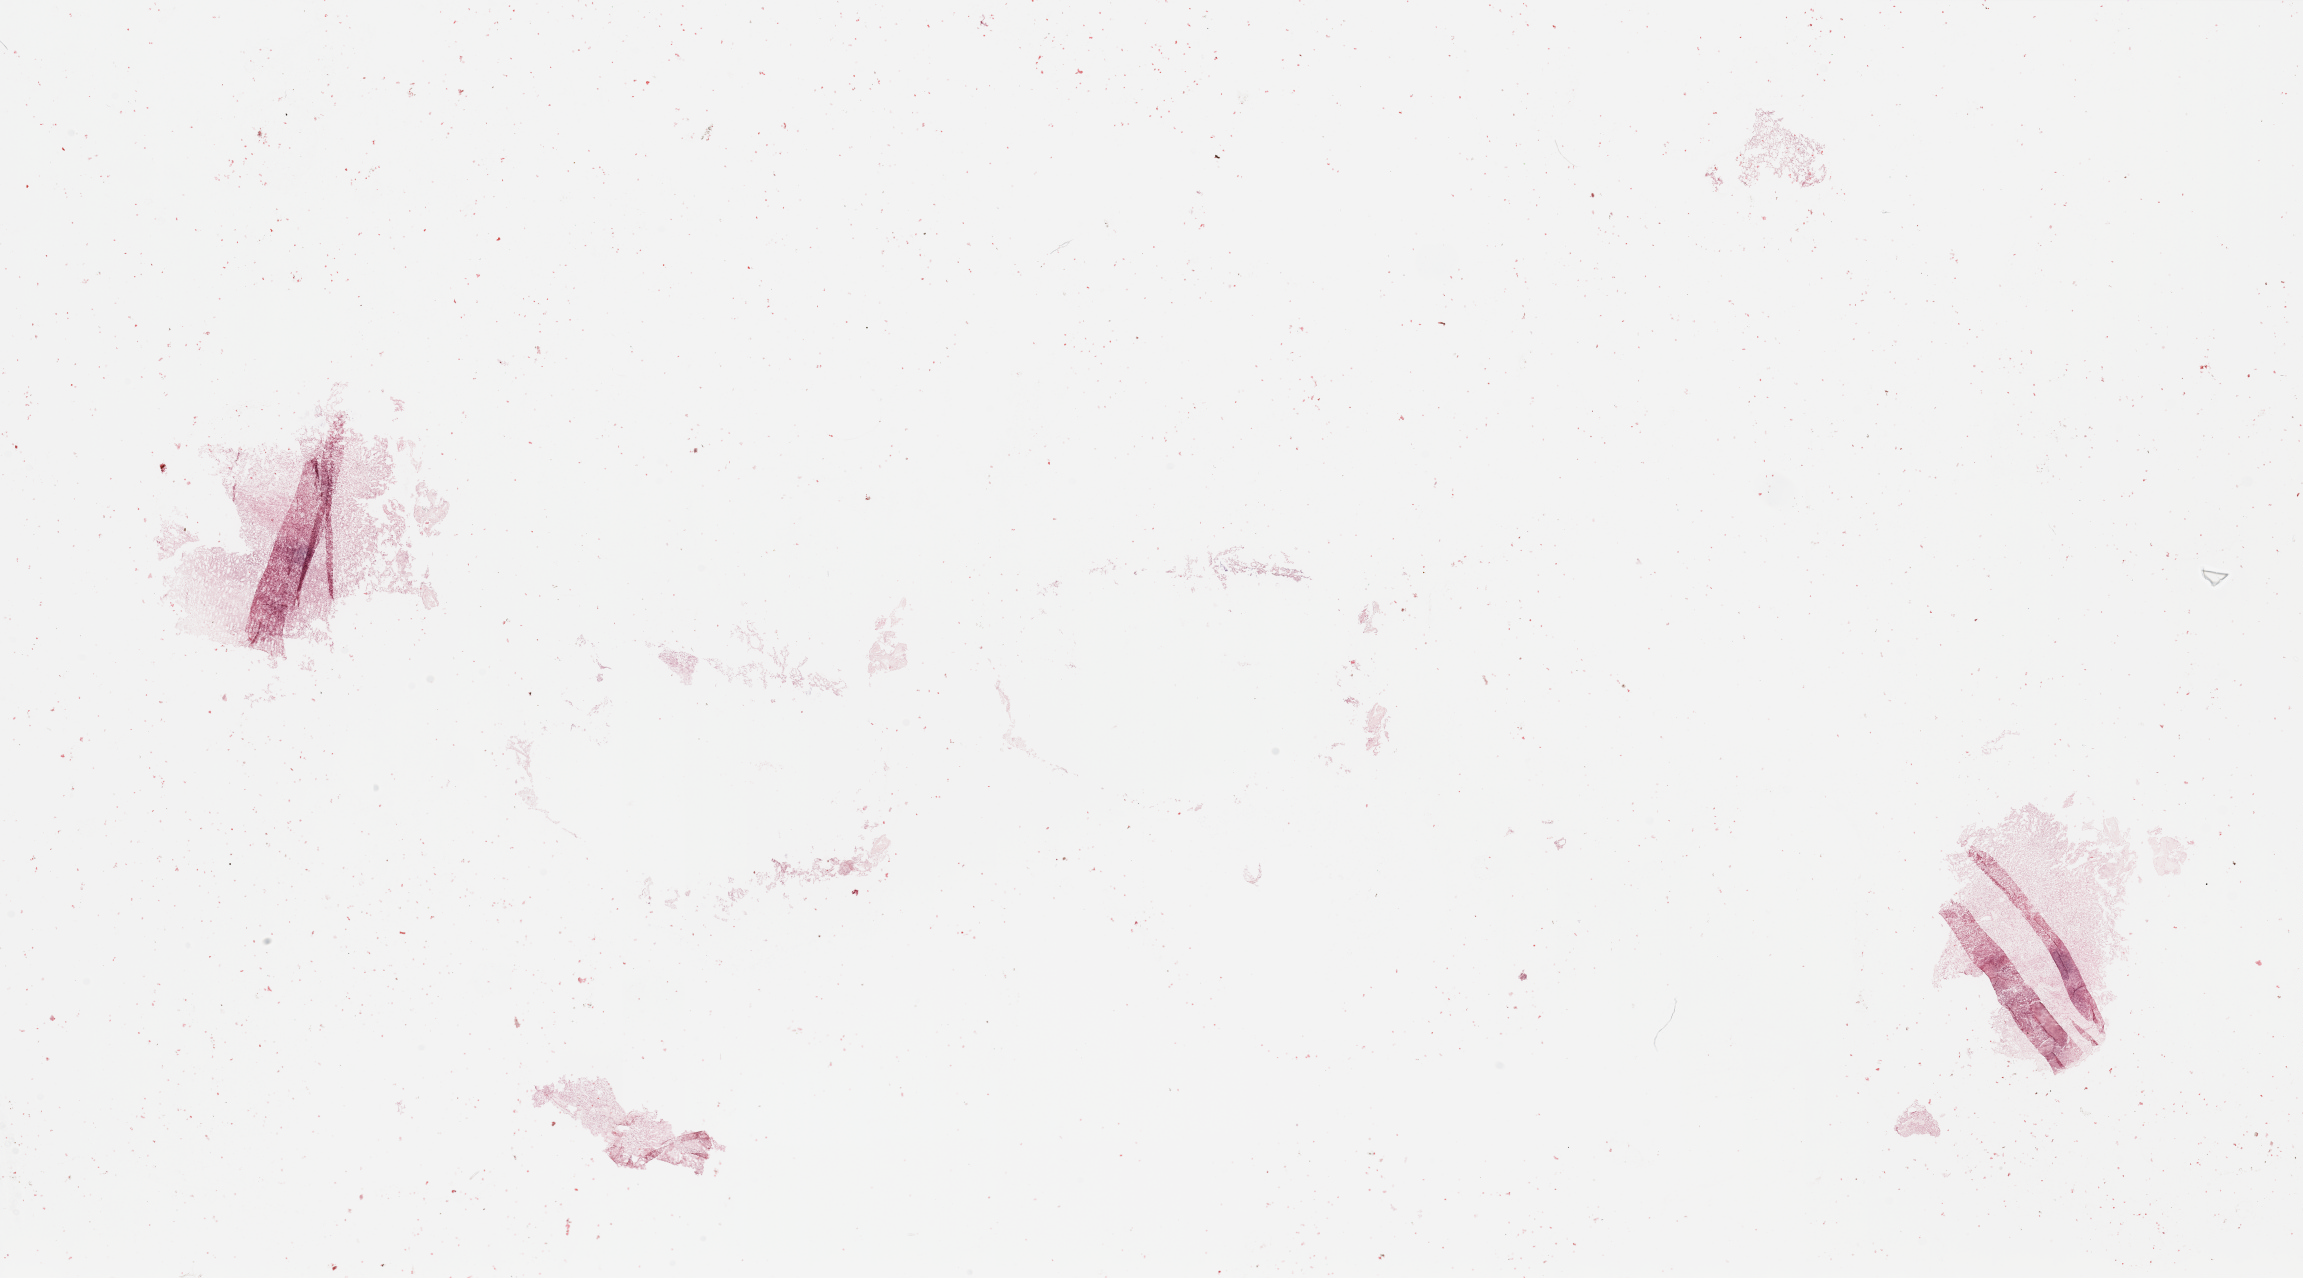
Whole-slide histology image, Hematoxylin and eosin (H&E) stained — whole scanned area (about 36.4 x 20.2 mm) shown as a low-resolution overview. Tumour tissue sample, sampled site: occipital cortex. Male, 66 y/o. Composition of this section per pathologist review: tumour nuclei 85%, necrosis 5%.
Primary tumour site (as recorded): occipital lobe. Diagnosis: Glioblastoma.